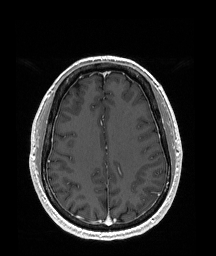
Brain MRI from a brain-tumour surgery series, one axial slice. Position 71 of 192 along the scan axis. T1-weighted post-contrast. 1 mm slice thickness. 216 × 256 image matrix. Case-level facts recorded for this patient, not image findings: histopathology: Glioblastoma; WHO grade: 4; IDH mutation: no; tumour location: Left Temporal Parietal.
Structures marked on this image (expert manual segmentation):
- tumour: box from (x=143, y=186) to (x=158, y=204) px